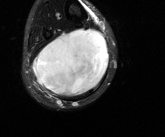
MRI of an extremity soft-tissue mass, one axial slice; slice 50 of 81 in the series (ordered by position); T2-weighted fat-saturated; MR volume resampled by the dataset authors to the PET/CT grid (not the native acquisition matrix); 3.27 mm slice thickness; 165 × 137 image matrix, field of view 161 × 134 mm. Male patient. Case-level facts recorded for this patient, not image findings: histological type: liposarcoma - round cell; grade: high; site of the primary tumour: right calf.
Outlined on this slice (expert contour drawn on MRI and transferred to this co-registered scan by the dataset authors):
- gross tumour volume (mass): bounding box [x1, y1, x2, y2] px = [32, 27, 109, 97]